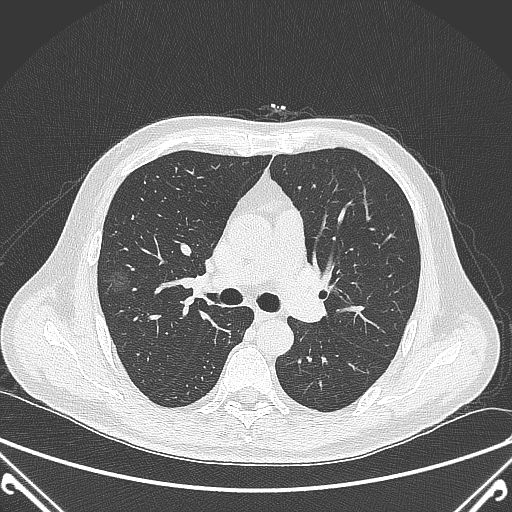
Chest CT, one axial slice; slice 228 of 360 in the series (ordered by position); 120 kVp; lung window (W 1500 / L -600 HU); 1 mm slice thickness; 512 × 512 image matrix, field of view 380 × 380 mm. Patient: male, 64 years. Case-level facts recorded for this patient, not image findings: clinical TNM (as recorded): T1c N0 M0; histopathological grade: G2.
Structures marked on this image (bounding box drawn by a radiologist):
- lung tumour (recorded histology: adenocarcinoma): bounding box [x1, y1, x2, y2] px = [105, 264, 140, 295]